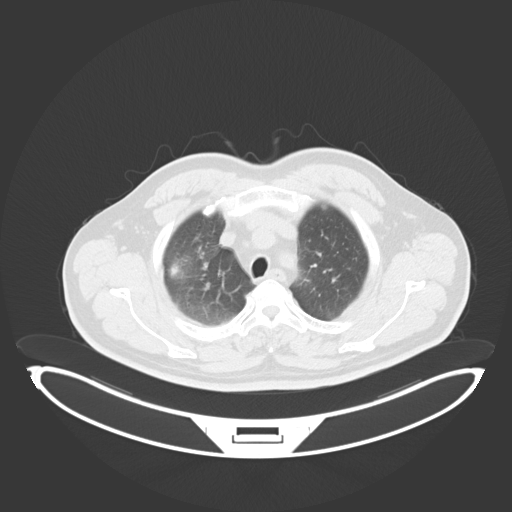
Chest CT, one axial slice. Slice 229 of 284 in the series (ordered by position). Reconstruction kernel B30f. Lung window (W 1500 / L -600 HU). 3 mm slice thickness. 512 × 512 image matrix, field of view 500 × 500 mm. Male patient, age 55 years. Case-level facts recorded for this patient, not image findings: clinical TNM (as recorded): T3 N2 M1.
Annotated regions visible in this slice (rectangle marked by the reading radiologist):
- lung tumour (recorded histology: adenocarcinoma): bounding box <167,259,188,286> (left, top, right, bottom; pixels)